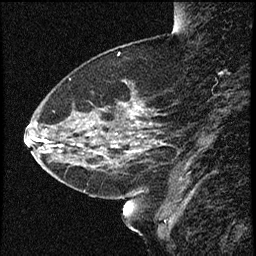
Breast MRI (dynamic contrast-enhanced), one sagittal slice; position 17 of 60 along the scan axis; dynamic contrast-enhanced study with each time point stored as its own series, time point 2 of 4 at this slice position (early post-contrast, ordered by acquisition time); 1.5 T; TE 4.2 ms, TR 16.7 ms; 2 mm slice thickness; 256 × 256 image matrix, field of view 200 × 200 mm. Female patient, age 52 years. From the clinical record (not read from this slice): setting: breast cancer imaged before/during neoadjuvant chemotherapy; receptor status: HER2-positive.
Annotated regions visible in this slice (semi-automatic segmentation, software-assisted and operator-edited):
- analysis volume of interest (the breast-tissue region the enhancement analysis was run in; not a lesion): box from (x=37, y=79) to (x=163, y=181) px
- tumour enhancement mask (voxels above the 100 % enhancement threshold inside the analysis volume of interest): (x=42, y=107)–(x=139, y=141)